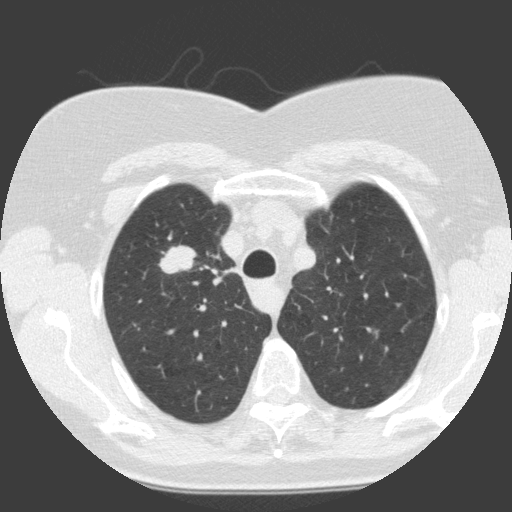
Low-dose screening chest CT, one axial slice; position 115 of 146 along the scan axis; 120 kVp; lung window (W 1500 / L -600 HU); 512 × 512 image matrix.
Annotated regions visible in this slice (manually delineated by an expert):
- lesion 1 (tumor, upper lobe of right lung): bounding box [x1, y1, x2, y2] px = [158, 245, 197, 274]